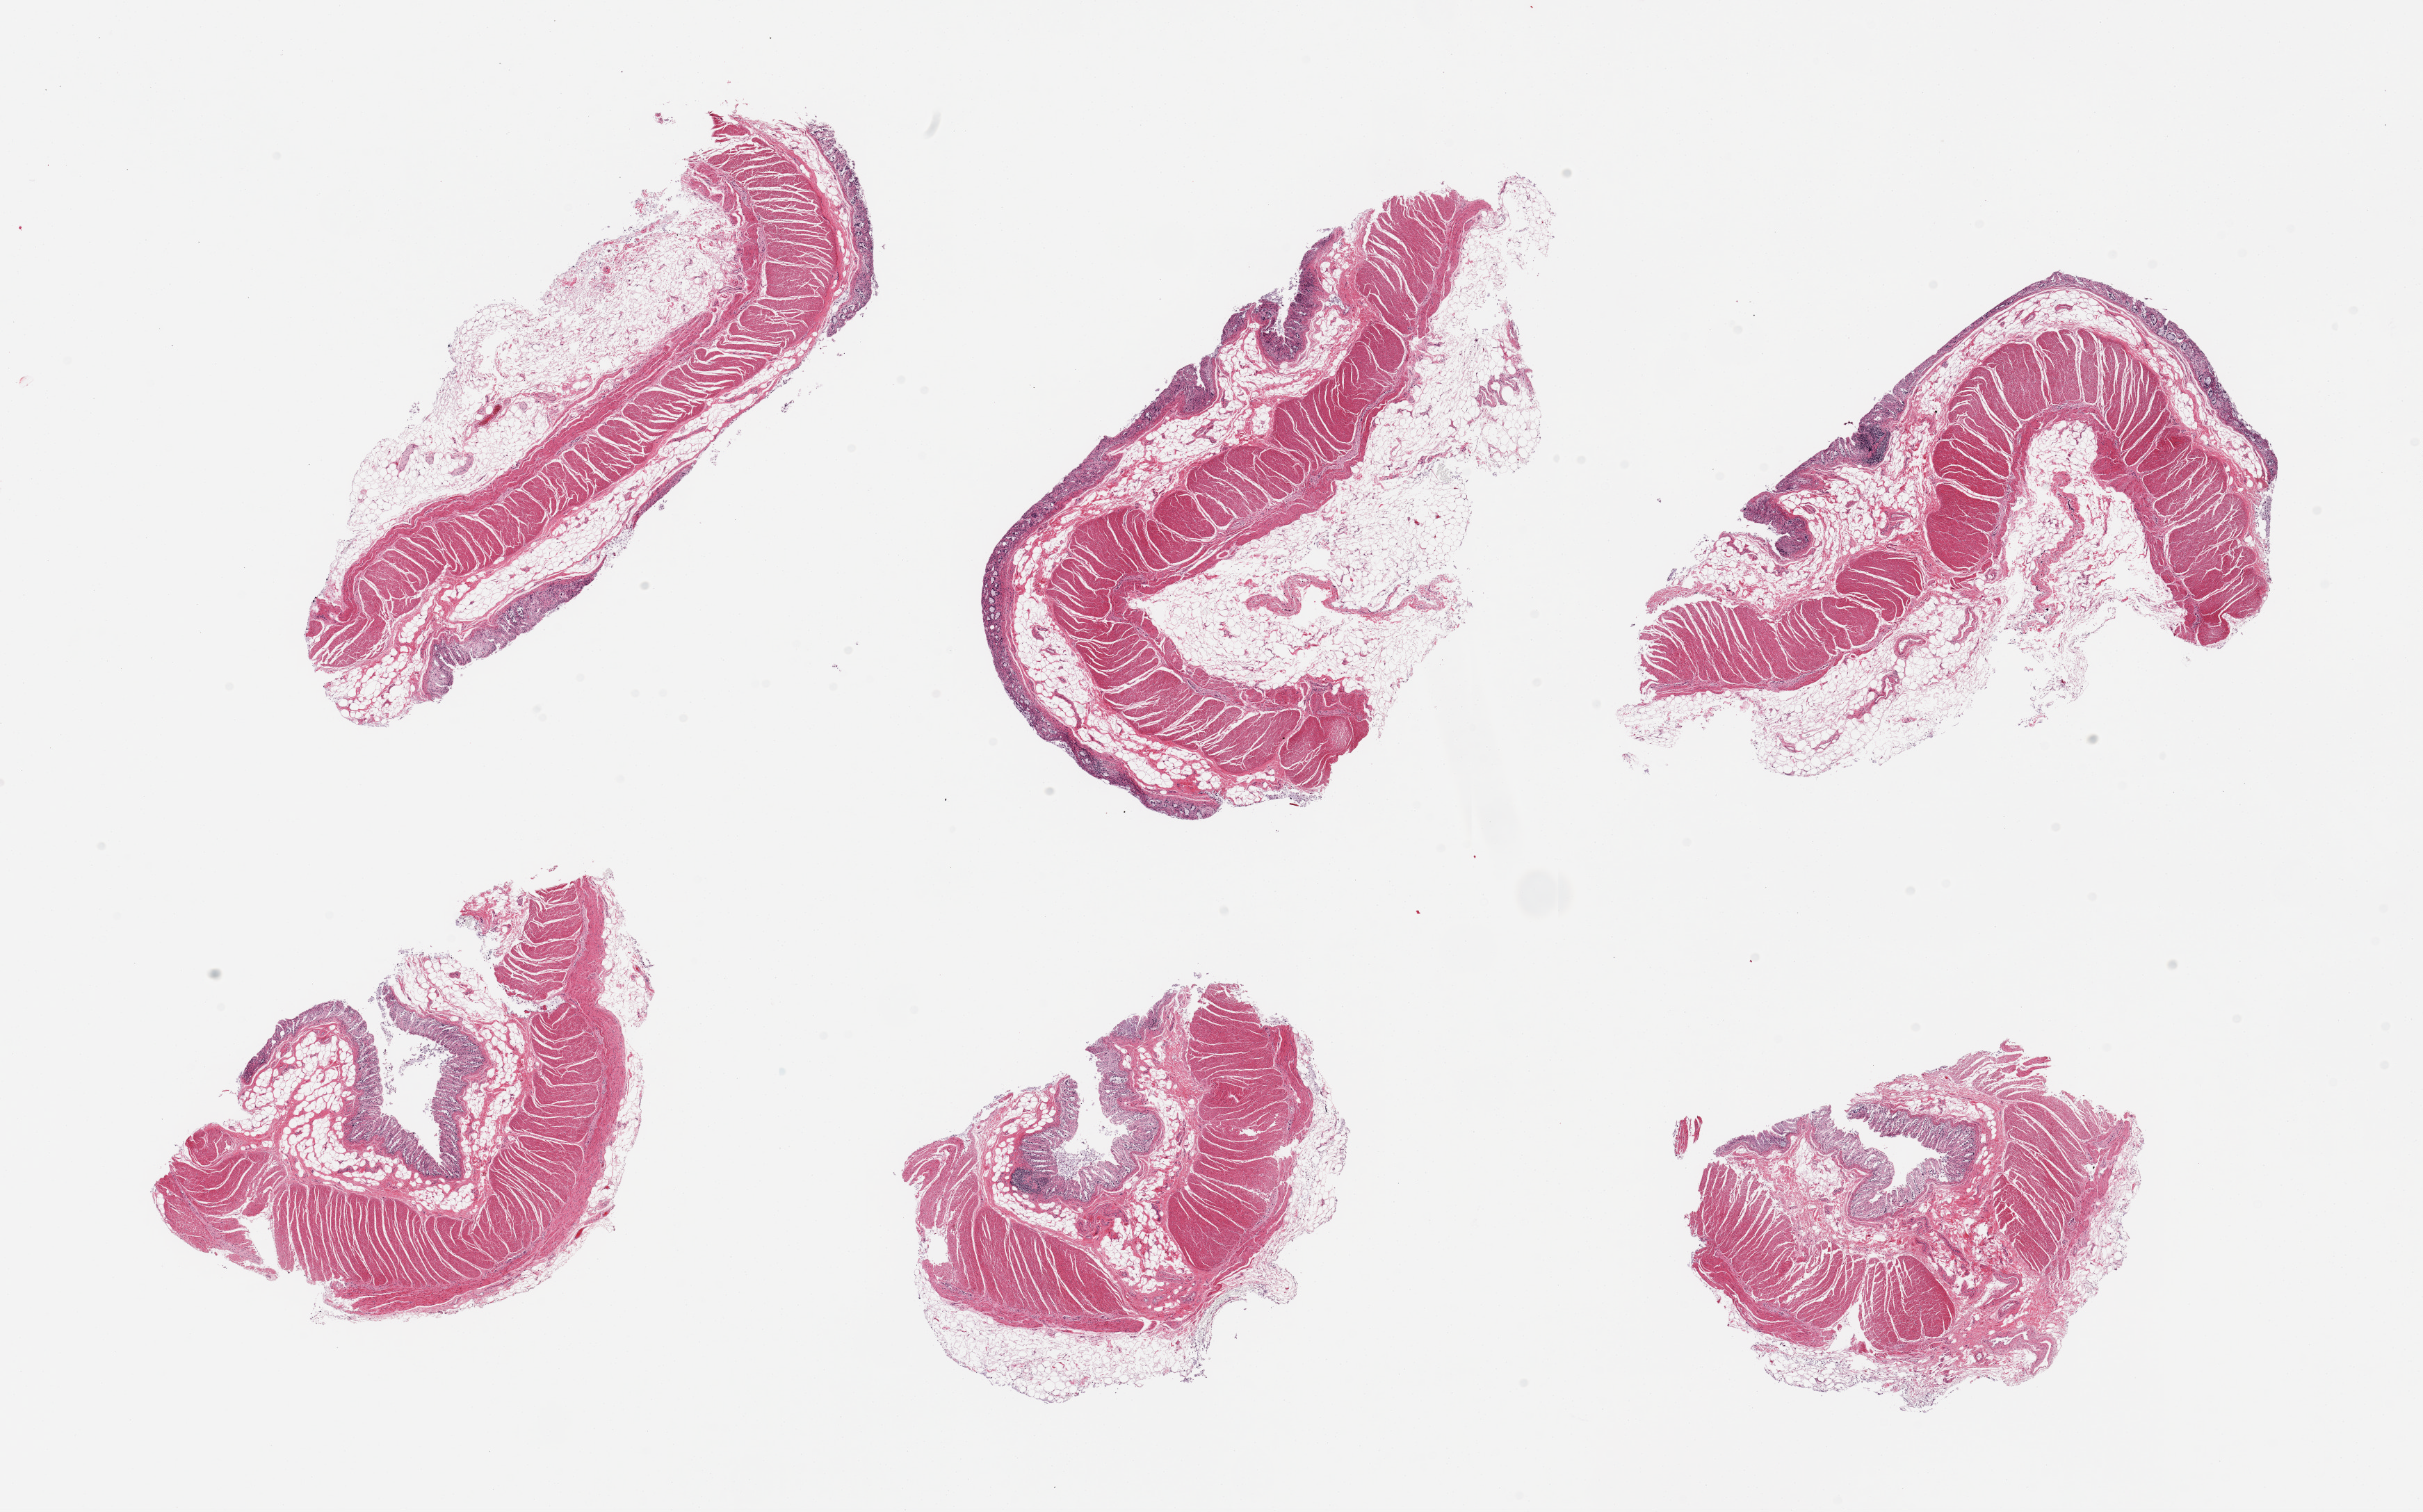
Haematoxylin and eosin whole-slide image, whole scanned area (about 27.6 x 17.2 mm, slide scanned at 20x) shown as a low-resolution overview, PAXgene-fixed paraffin-embedded (PFPE) section, sampled site (target tissue): sigmoid colon, donor tissue sample. Donor sex: male.
Review note (as recorded): 6 pieces; all include residual moderately autolyzed mucosa (not target) and attached fat.